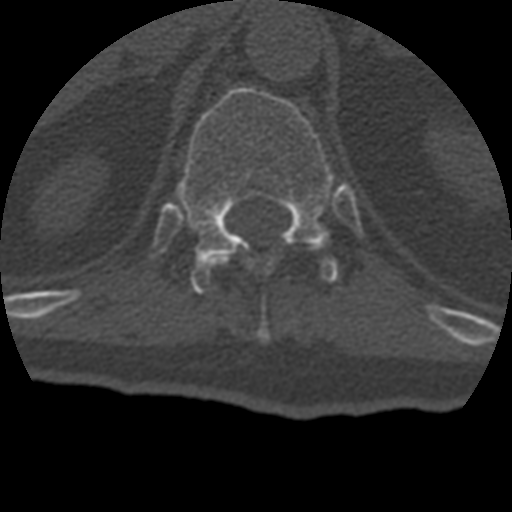
CT including the spine, one axial slice. Slice 182 of 399 in the series (ordered by position). Bone window (W 1800 / L 400 HU). 1.25 mm slice thickness. 512 × 512 image matrix. Patient age 69 years. From the clinical record (not read from this slice): primary cancer: prostate.
Annotated regions visible in this slice (semi-automatic segmentation, software-assisted and operator-edited):
- T11 vertebra: bounding box <212,245,309,341> (left, top, right, bottom; pixels)
- T12 vertebra: <176,87,339,291>